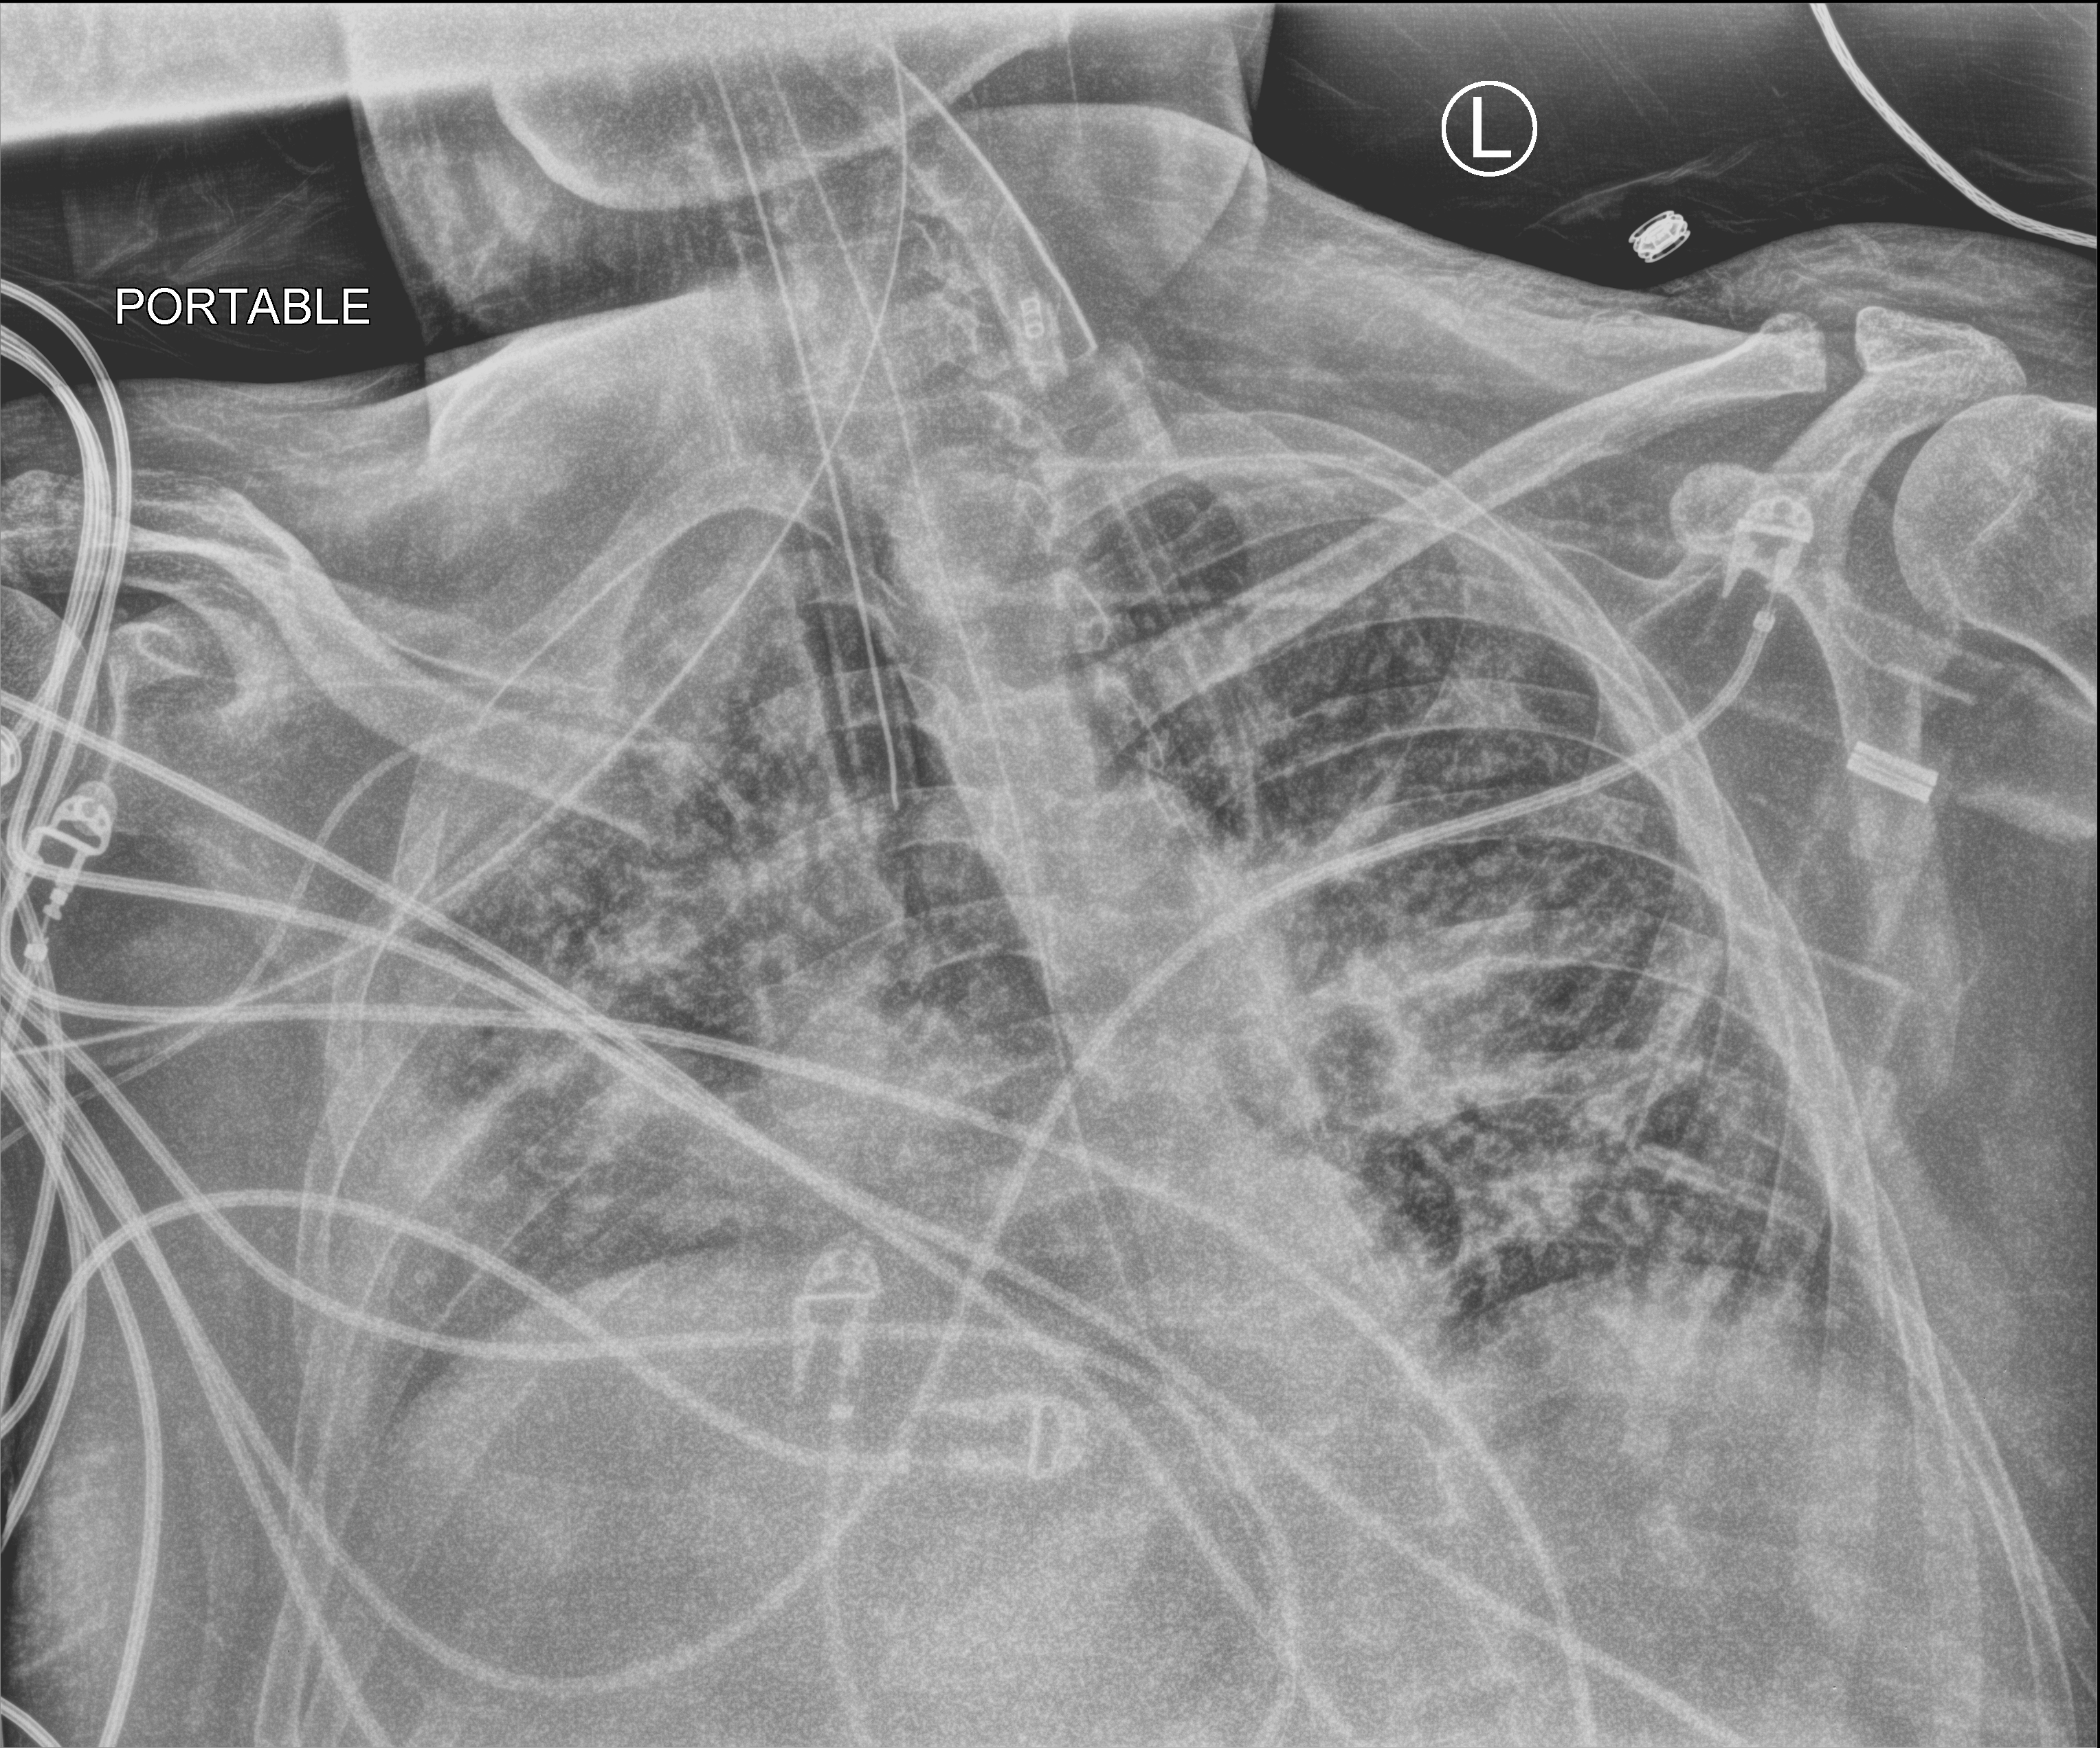
Bedside chest radiograph (computed radiography), anteroposterior (AP) projection. Patient hospitalised with COVID-19, aged 18–59 years.
From the hospital-stay record, not from the radiograph (when in the stay this image was taken is not recorded): length of hospital stay: 50 days; admitted to intensive care during this hospital stay: yes; other chronic lung disease (admission record): yes.